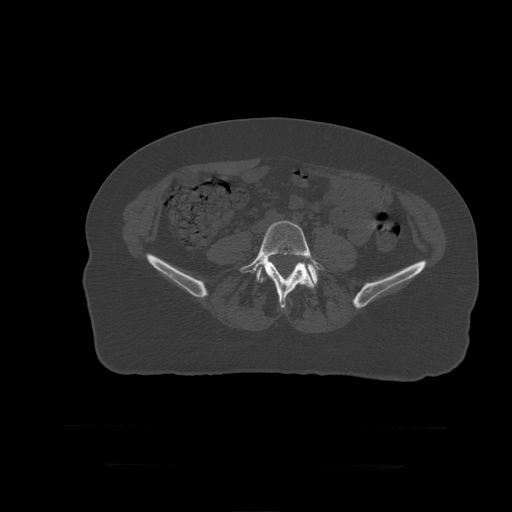
CT including the spine, one axial slice; slice 73 of 399 in the series (ordered by position); reconstruction kernel STANDARD; 120 kVp; bone window (W 1800 / L 400 HU); 512 × 512 image matrix. Patient age 41 years. Case-level facts recorded for this patient, not image findings: primary cancer: breast.
Annotated regions visible in this slice (semi-automatic segmentation, software-assisted and operator-edited):
- L5 vertebra: box from (x=240, y=220) to (x=325, y=309) px